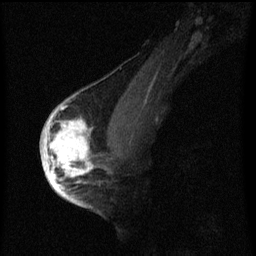
Breast MRI (dynamic contrast-enhanced), one sagittal slice; slice 39 of 60 in the series (ordered by position); dynamic contrast-enhanced series, image 2 of 3 at this slice position (ordered by acquisition); 1.5 T; TE 4.2 ms, TR 8 ms; 256 × 256 image matrix, field of view 180 × 180 mm. Patient: female, 56 years.
Outlined on this slice (semi-automatic segmentation, software-assisted and operator-edited):
- analysis volume of interest (the breast-tissue region the enhancement analysis was run in; not a lesion): box from (x=42, y=110) to (x=101, y=193) px
- tumour enhancement mask (voxels above the 70 % enhancement threshold inside the analysis volume of interest): (x=42, y=110)–(x=93, y=193)